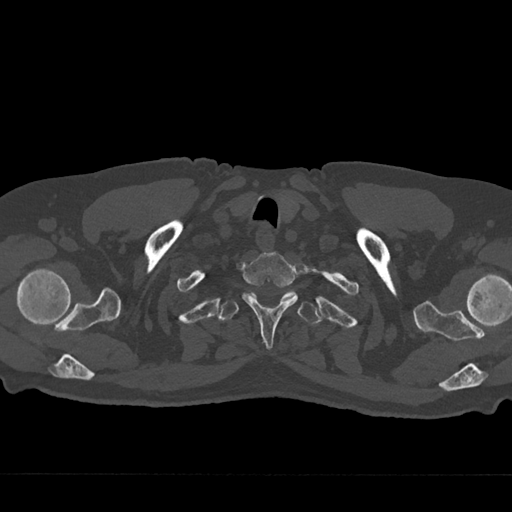
CT including the spine, one axial slice. Slice 645 of 797 in the series (ordered by position). 120 kVp. Bone window (W 1800 / L 400 HU). 0.5 mm slice thickness. 512 × 512 image matrix. Patient: male, 75 years. From the clinical record (not read from this slice): primary cancer: renal.
Structures marked on this image (semi-automatically segmented with operator editing):
- T1 vertebra: bounding box <242,253,298,349> (left, top, right, bottom; pixels)
- T2 vertebra: <218,290,321,325>